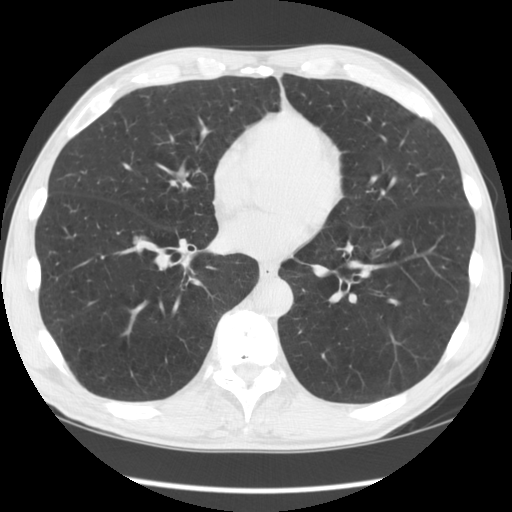
Low-dose screening chest CT, axial slice. Second screening round (one year after baseline). Lung window (W 1500 / L -600 HU). 2.5 mm slice thickness. Standard (soft-tissue) reconstruction kernel (STANDARD). 120 kVp. Slice 87 of 135 in the series. Male, age 60 years at enrolment.
Lesion marked by an expert reader, bounding box [x1, y1, x2, y2] px = [112, 223, 159, 267]. Reader record for this screening exam (exam-level; its link to the box is not recorded): non-calcified nodule or mass ≥4 mm, right lower lobe, 17 × 14 mm, smooth margins, soft tissue attenuation, pre-existing on the prior screen: yes; interval growth: yes. Official screen result: positive, other. Later outcome: lung cancer diagnosed 39 days after this screen — large cell carcinoma, NOS, right lower lobe, undifferentiated (G4), stage IA (AJCC 6th edition), 16 mm at pathology.